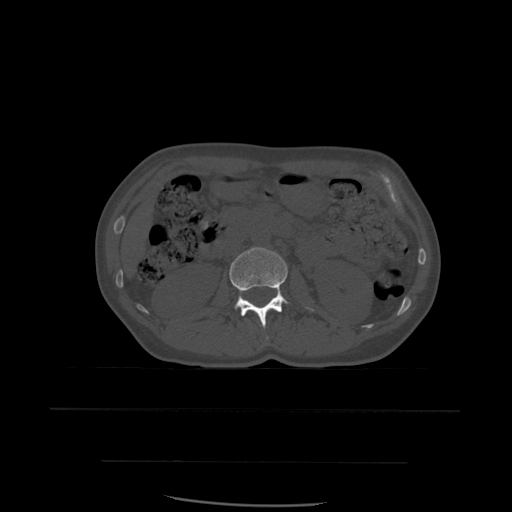
CT including the spine, one axial slice; position 224 of 574 along the scan axis; bone window (W 1800 / L 400 HU); 1.25 mm slice thickness; 512 × 512 image matrix, field of view 392 × 392 mm. Patient age 48 years. From the clinical record (not read from this slice): primary cancer: lung; vertebrae with lytic lesions (as recorded): T11.
Outlined on this slice (semi-automatically segmented with operator editing):
- L2 vertebra: bounding box [x1, y1, x2, y2] px = [230, 248, 315, 328]